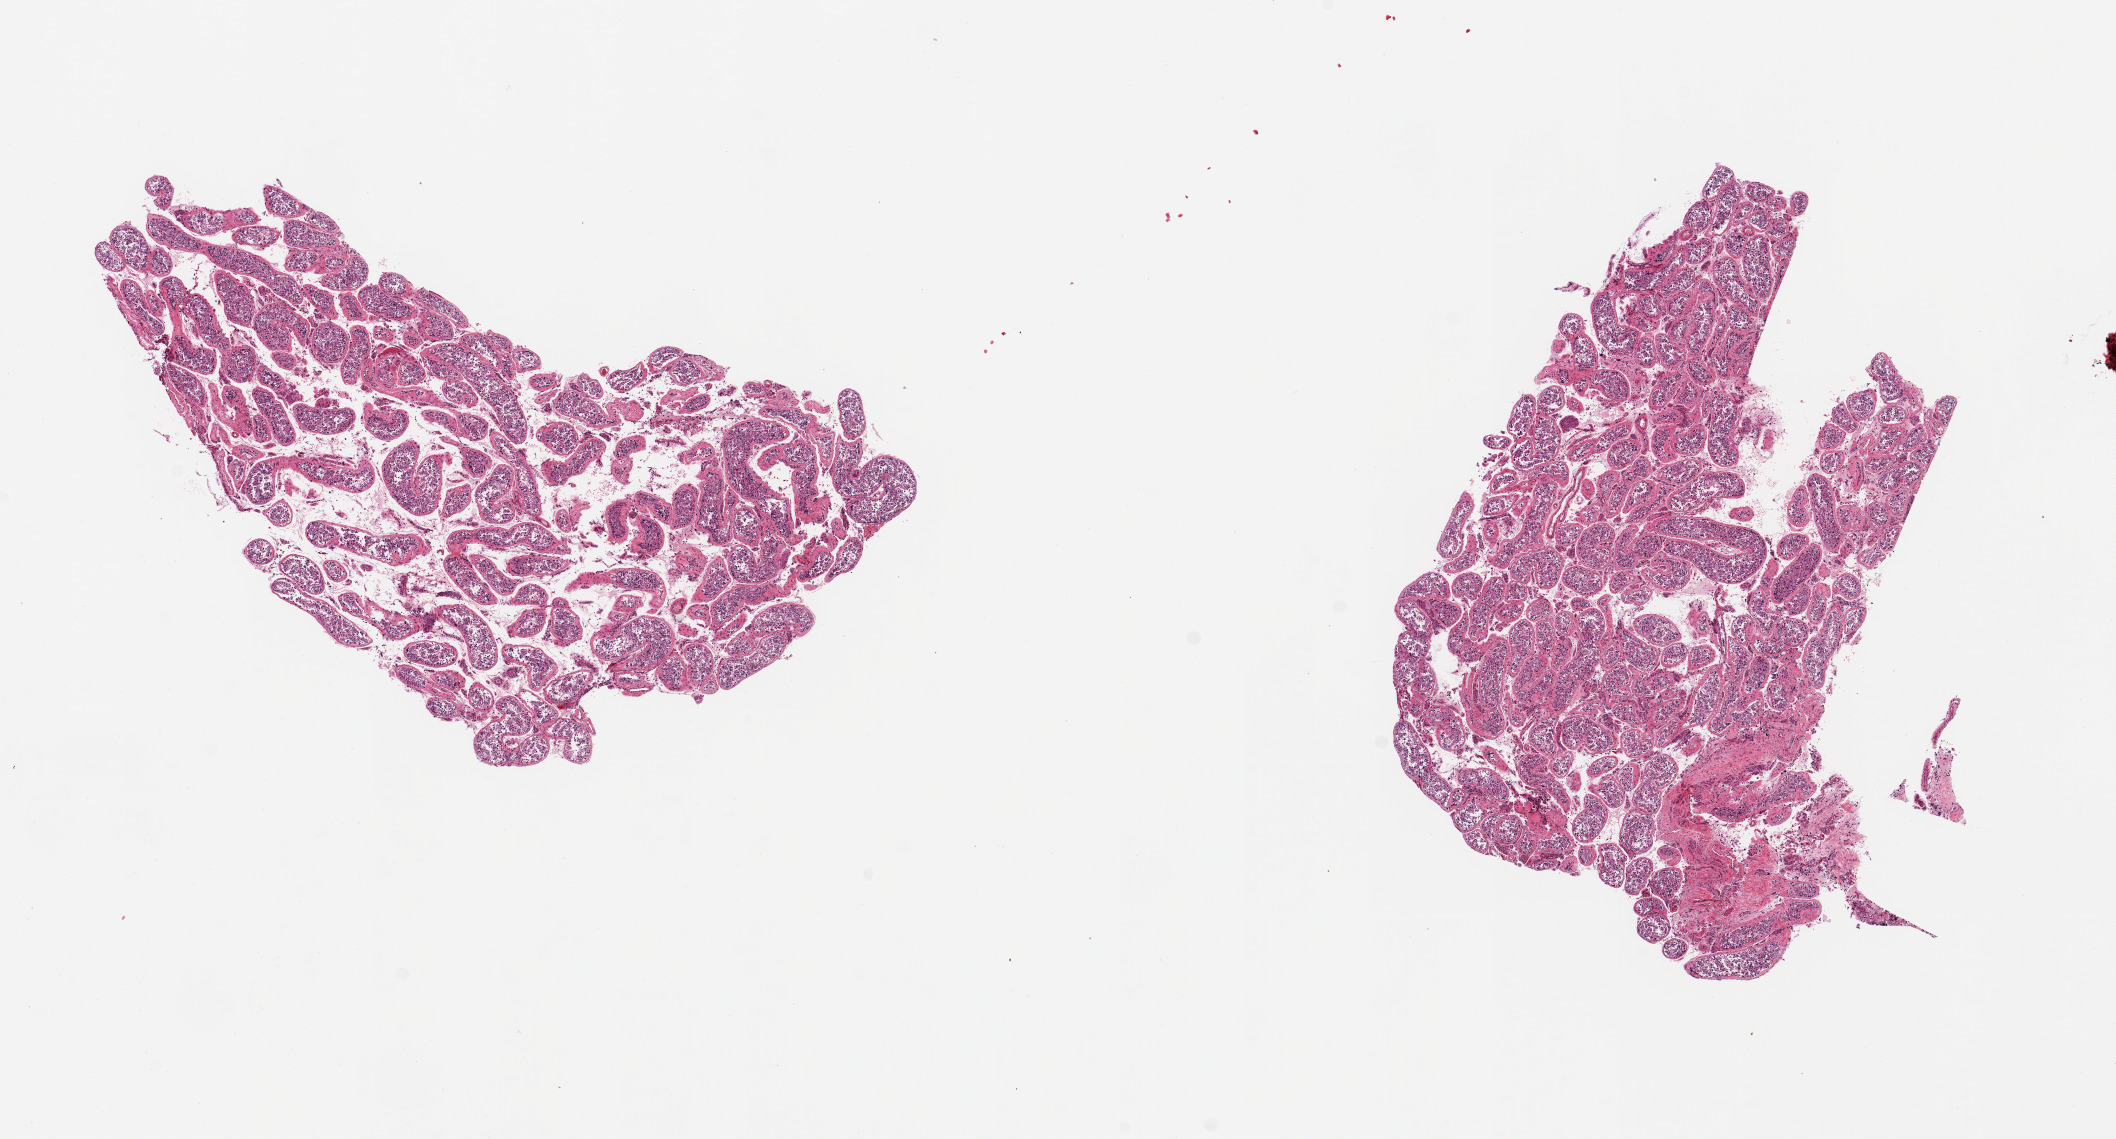
Hematoxylin and eosin (H&E) whole-slide image, brightfield, low-resolution overview of the scanned area, about 16.7 x 9.0 mm (acquisition: 20x scan). PAXgene-fixed, paraffin-embedded tissue. Section of testis (target tissue). Tissue donor sample. Male donor.
* review note (as recorded): 2 pieces, 6x4 & 6x5mm; reduced sperm maturation